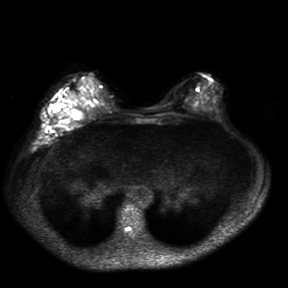
Breast MRI, one axial slice; slice 15 of 30 in the series (ordered by position); diffusion-weighted series; image 2 of 4 stored at this slice position (different b-values; order by instance number); 3 T; 4 mm slice thickness; 288 × 288 image matrix, field of view 360 × 360 mm. Female patient.
Outlined on this slice (expert manual segmentation):
- tumour on diffusion-weighted imaging: bounding box <53,104,85,122> (left, top, right, bottom; pixels)